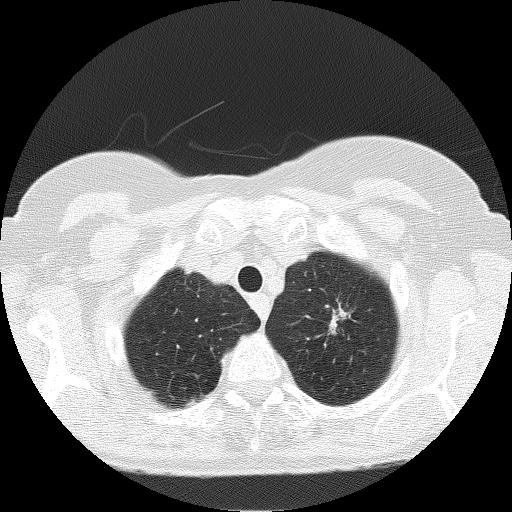
Axial slice from a low-dose chest CT screening exam, baseline annual screen, lung window (W 1500 / L -600 HU), 2 mm slice thickness. Female participant, aged 66 years at enrolment. Current smoker at enrolment.
Lesion marked by an expert reader, bounding box [x1, y1, x2, y2] px = [311, 284, 373, 354]. The screening reader recorded 3 non-calcified nodules or masses ≥4 mm on this exam (left upper lobe, left upper lobe, left upper lobe); which of them this box marks is not recorded. Lung cancer was diagnosed 156 days after this screen: adenocarcinoma, NOS, left upper lobe, moderately differentiated (G2), stage IB (AJCC 6th edition), 17 mm at pathology.